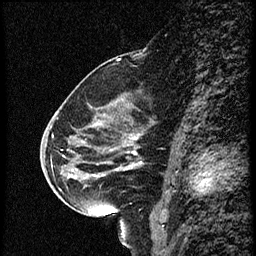
Breast MRI (dynamic contrast-enhanced), one sagittal slice; position 32 of 56 along the scan axis; dynamic contrast-enhanced study with each time point stored as its own series, time point 2 of 4 at this slice position (early post-contrast, ordered by acquisition time); 1.5 T; TE 4.2 ms, TR 18.9 ms; 2 mm slice thickness; 256 × 256 image matrix, field of view 200 × 200 mm. Female patient. From the clinical record (not read from this slice): setting: breast cancer imaged before/during neoadjuvant chemotherapy; receptor status: HER2-positive.
Annotated regions visible in this slice (semi-automatically segmented with operator editing):
- analysis volume of interest (the breast-tissue region the enhancement analysis was run in; not a lesion): bounding box [x1, y1, x2, y2] px = [63, 80, 161, 215]
- tumour enhancement mask (voxels above the 100 % enhancement threshold inside the analysis volume of interest): [95, 168, 129, 177]